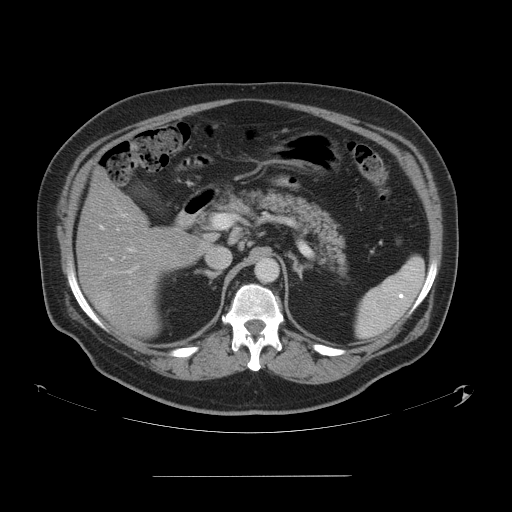
Contrast-enhanced abdominal CT, one axial slice. Slice 30 of 58 in the series (ordered by position). Intravenous contrast given. Soft-tissue window (W 400 / L 40 HU). 5 mm slice thickness. 512 × 512 image matrix, field of view 480 × 480 mm. Male patient, age 63 years. Case-level facts recorded for this patient, not image findings: diagnosis: colorectal cancer liver metastases, imaged before liver resection; multiple liver metastases: no; largest metastasis: 4.2 cm.
Structures marked on this image (manually delineated by an expert):
- hepatic veins: box from (x=109, y=269) to (x=134, y=296) px
- liver: (x=77, y=172)–(x=202, y=335)
- planned liver remnant (the part of the liver to remain after resection): (x=78, y=182)–(x=202, y=335)
- portal vein (with intrahepatic branches): (x=100, y=226)–(x=138, y=284)